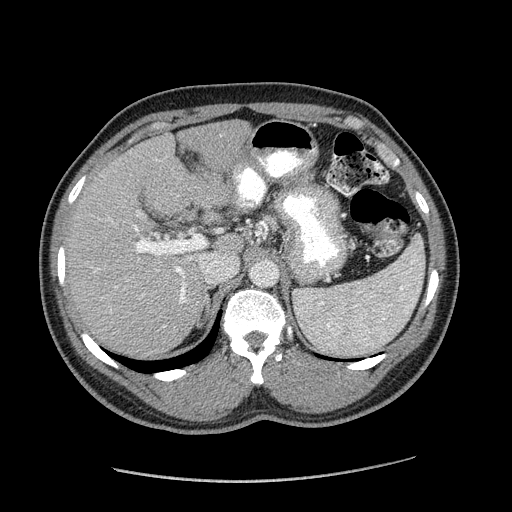
Contrast-enhanced abdominal CT (liver protocol), one axial slice; position 119 of 182 along the scan axis; 120 kVp; soft-tissue window (W 400 / L 40 HU); 2.5 mm slice thickness; 512 × 512 image matrix, field of view 400 × 400 mm. Case-level facts recorded for this patient, not image findings: diagnosis: hepatocellular carcinoma (patient treated with transarterial chemoembolisation; whether this scan precedes or follows treatment is not stated here); TNM stage (as recorded): Stage-I; Child-Pugh class: A; tumour nodularity: uninodular; tumour size: 3.1 cm.
Structures marked on this image (semi-automatically segmented with operator editing):
- liver parenchyma outside the tumour (the mass and vessels are separate outlines, so this box may not span the whole liver): box from (x=66, y=120) to (x=250, y=356) px
- liver vessels: (x=98, y=225)–(x=213, y=304)